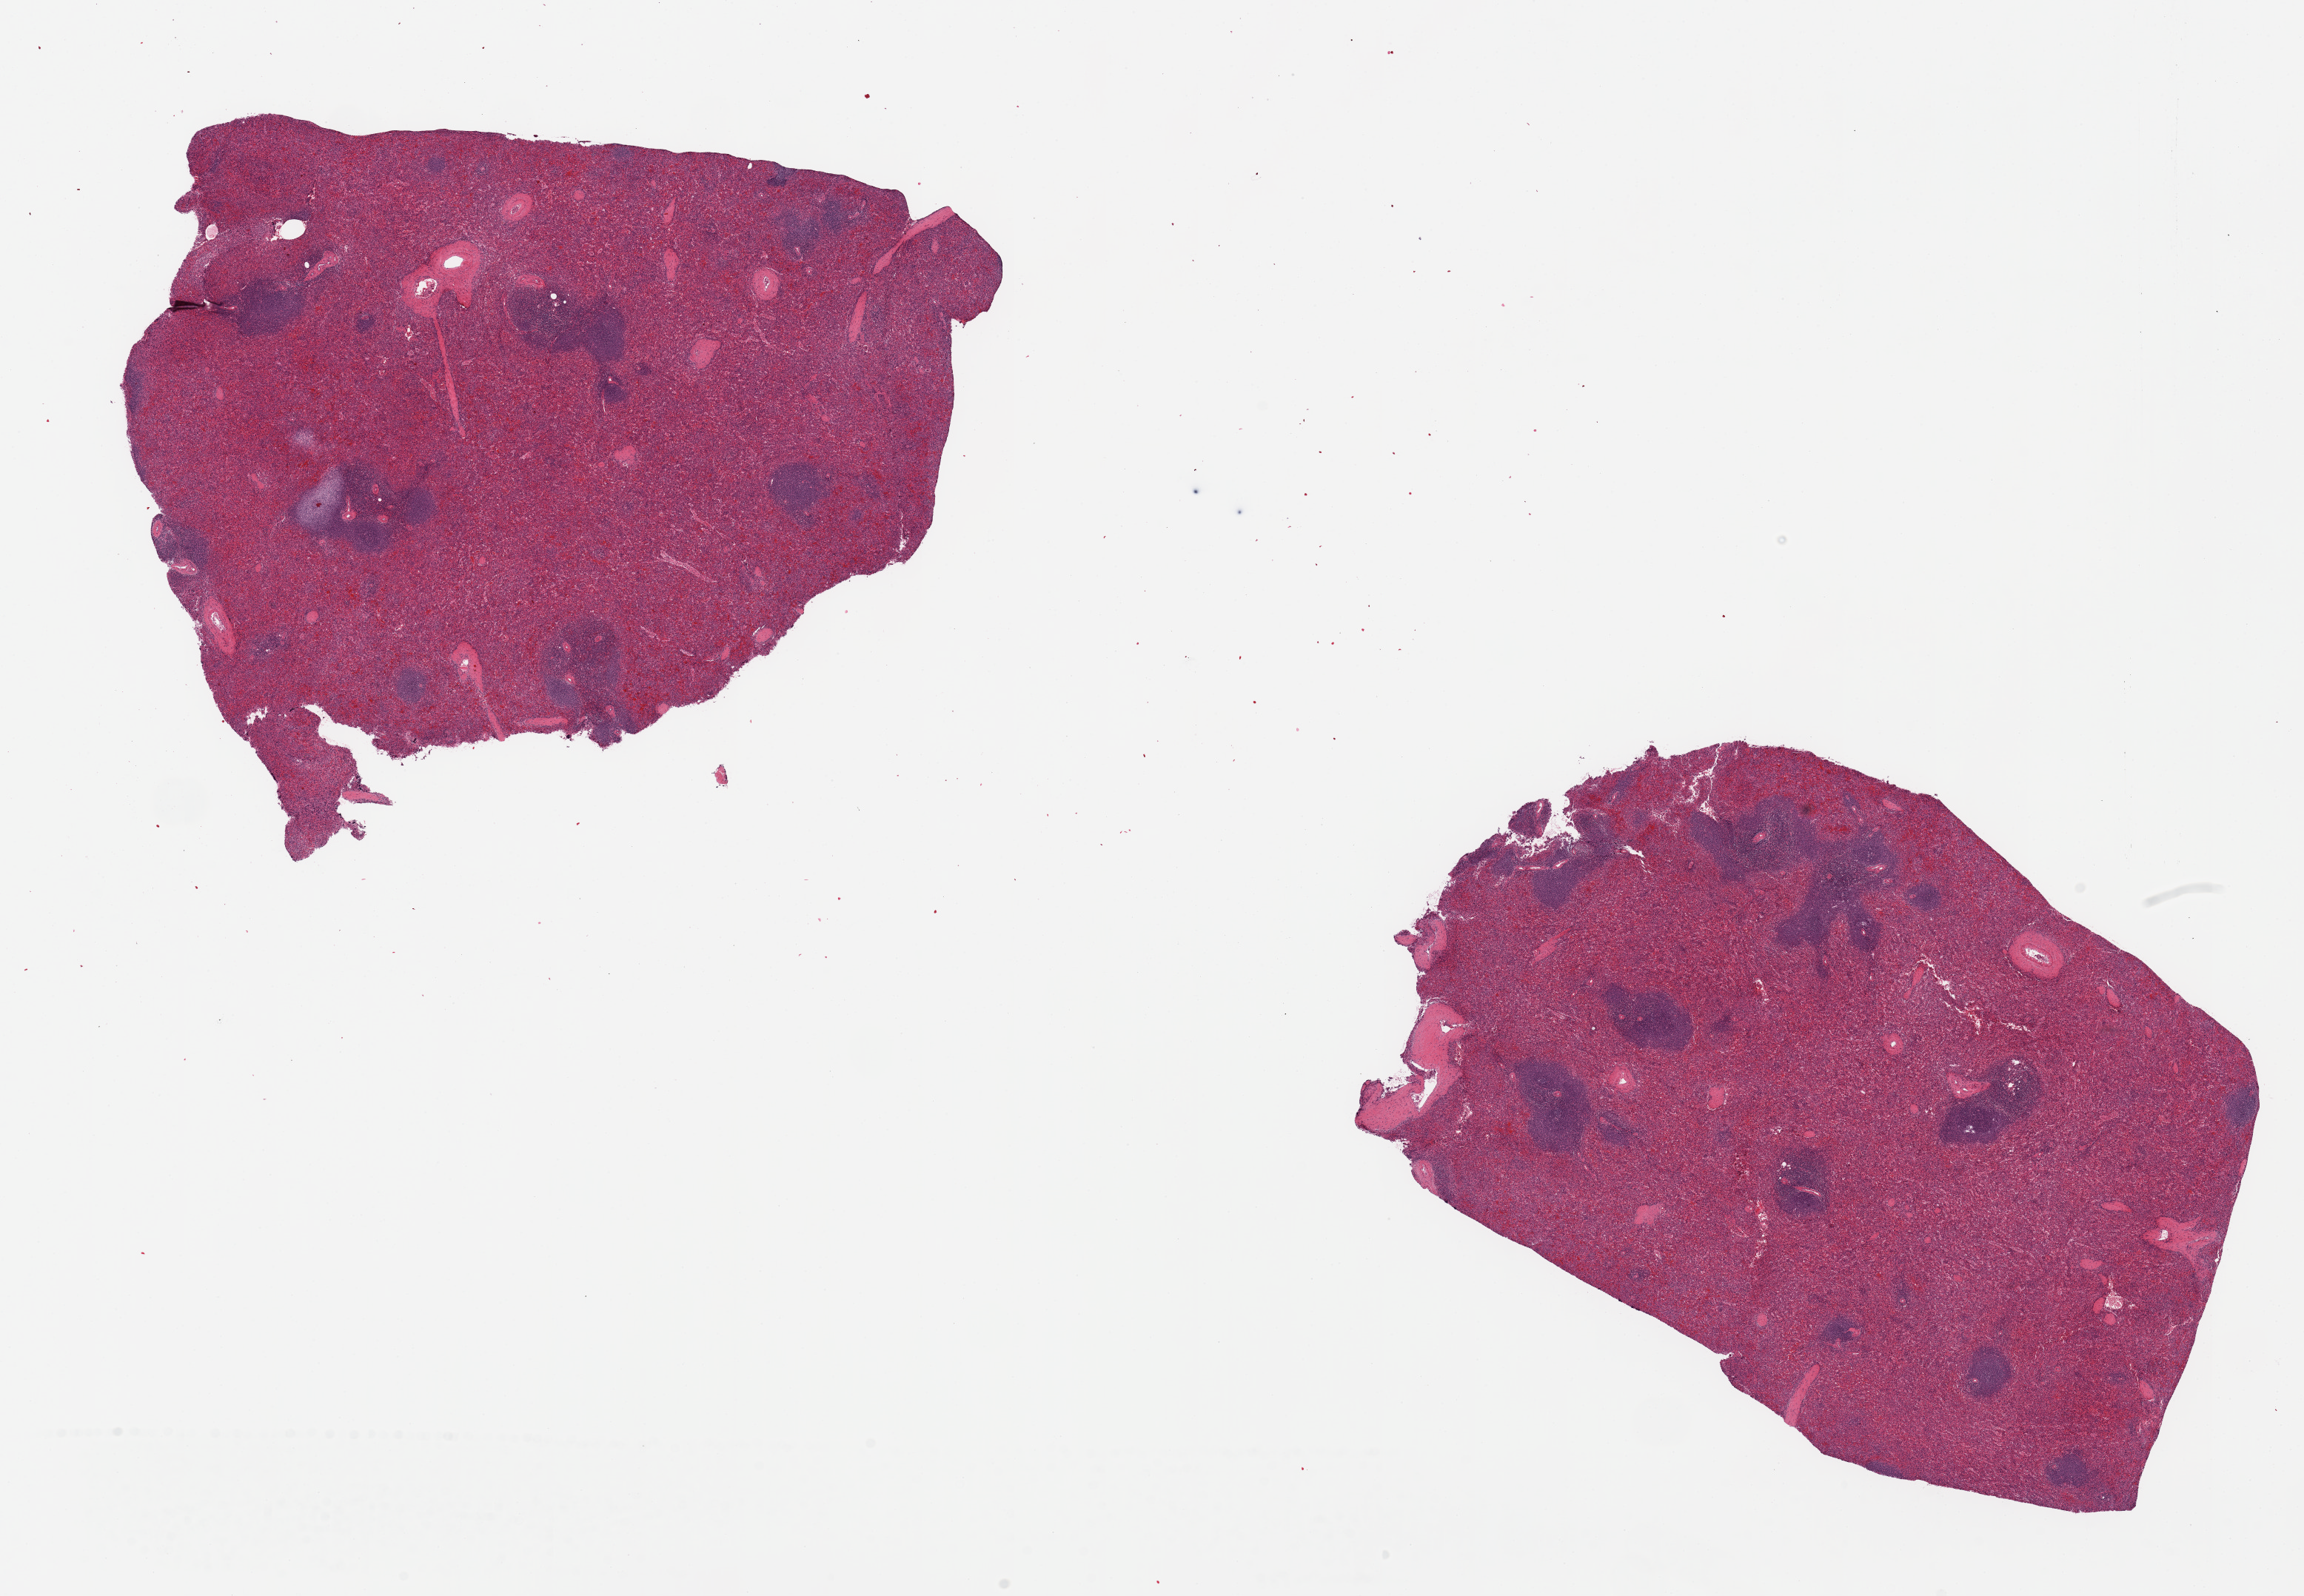
Haematoxylin and eosin whole-slide image, brightfield, shown as a low-resolution overview of the whole scanned area (about 24.6 x 17.1 mm, slide scanned at 20x), PAXgene-fixed paraffin-embedded (PFPE) section, target tissue: spleen, donor tissue sample. Donor sex: male.
- pathologist's review note for this sample: 2 pieces